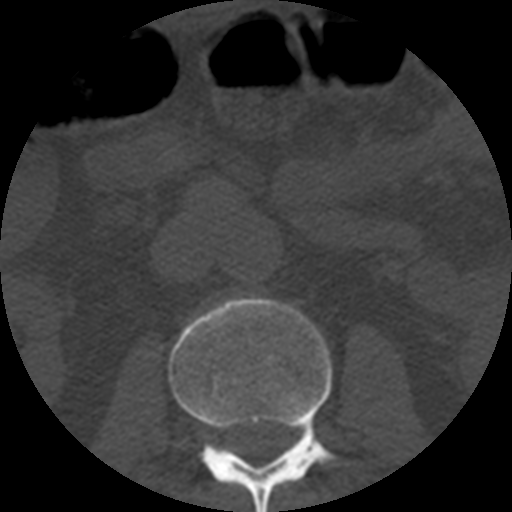
CT including the spine, one axial slice. Slice 148 of 508 in the series (ordered by position). Reconstruction kernel STANDARD. 120 kVp. Bone window (W 1800 / L 400 HU). 1.25 mm slice thickness. 512 × 512 image matrix, field of view 160 × 160 mm. Patient age 57 years. From the clinical record (not read from this slice): primary cancer: prostate.
Outlined on this slice (semi-automatic segmentation, software-assisted and operator-edited):
- L2 vertebra: box from (x=169, y=297) to (x=336, y=512) px